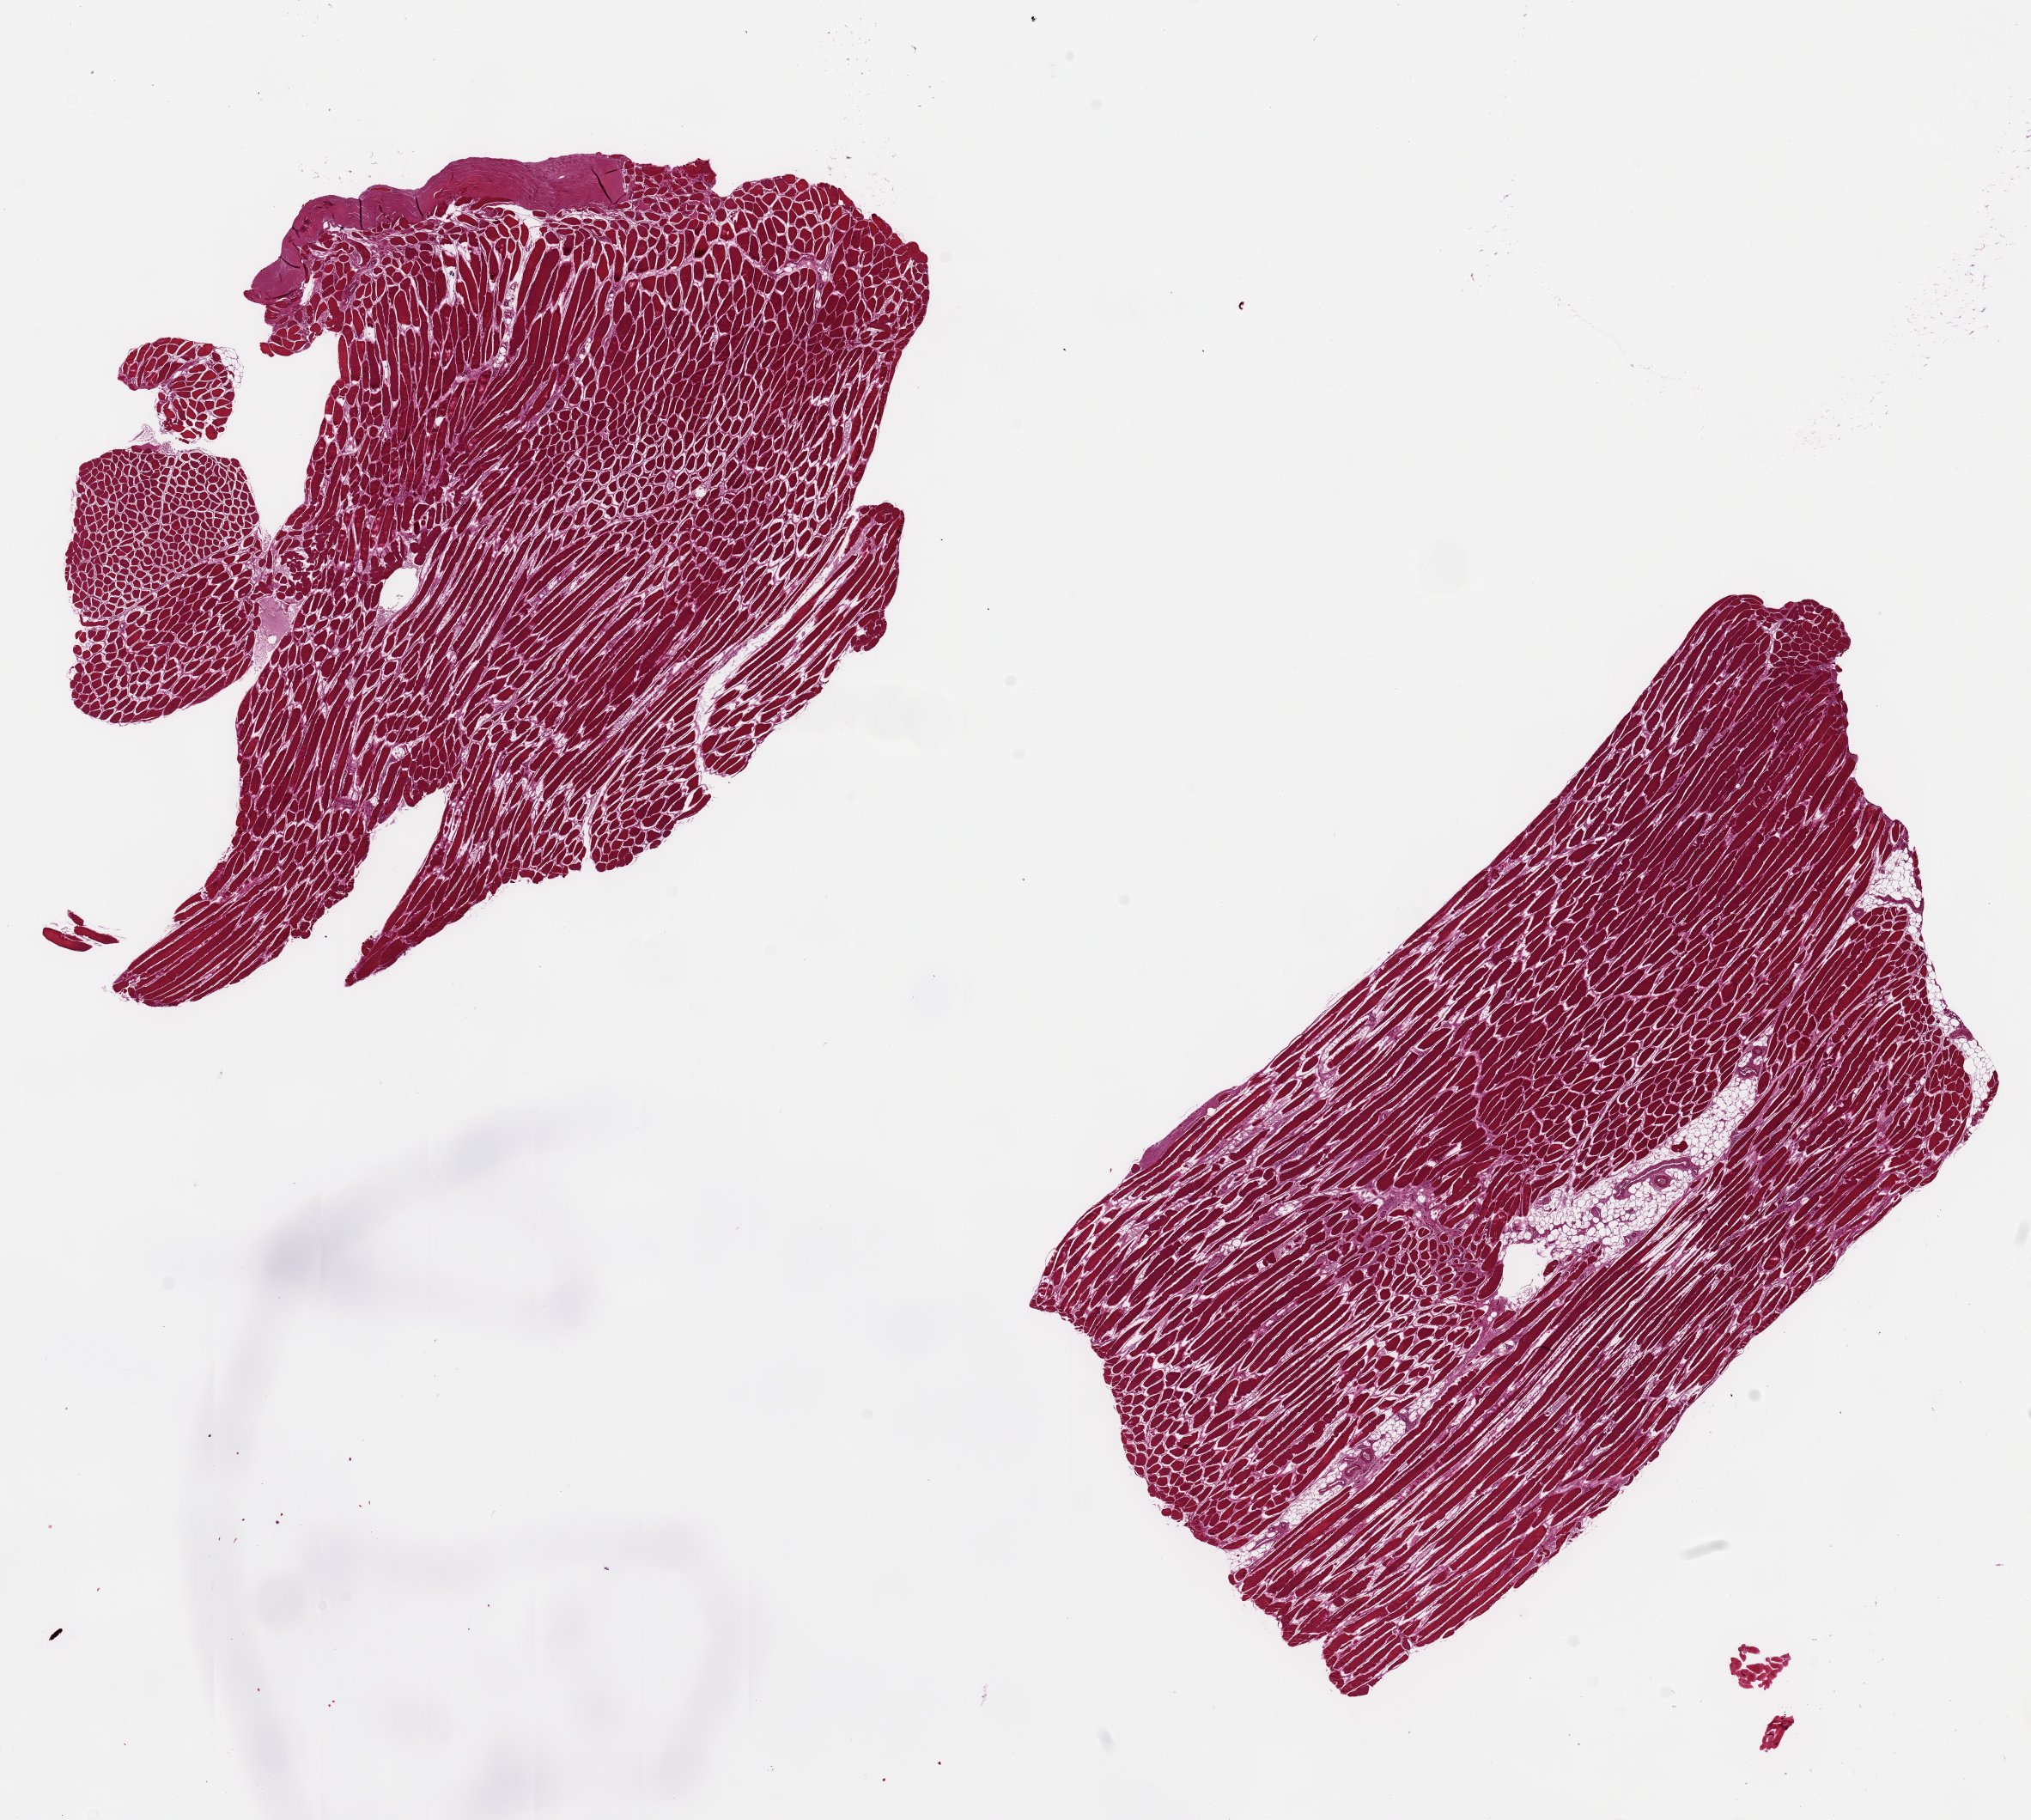
Digitized haematoxylin and eosin-stained section, a low-resolution overview of the entire scanned area, about 18.7 x 16.8 mm (slide scanned at 20x); PAXgene-fixed, paraffin-embedded tissue; section of skeletal muscle (target tissue); tissue donor sample. Male donor.
Reviewer comment on this tissue sample: 2 pieces, 8x7.5 & 9x5mm; <5% interstitial fat (focal), unusually badly autolyzed.